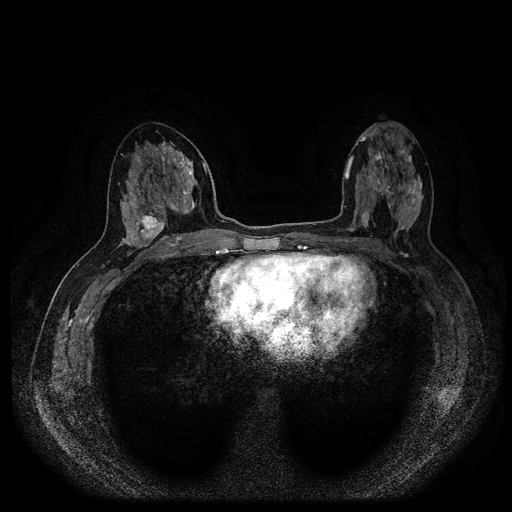
Breast MRI (dynamic contrast-enhanced, multi-phase), one axial slice; dynamic contrast-enhanced series, time point 2 of 5 at this slice position (early post-contrast); 1.5 T; TE 2.6 ms, TR 5.4 ms; 2 mm slice thickness; 512 × 512 image matrix, field of view 340 × 340 mm. Patient: female, 48 years.
Structures marked on this image (semi-automatic segmentation, software-assisted and operator-edited):
- breast lesion (labelled 'tumour' in the annotation; benign lesions carry a separate 'benign' label): box from (x=136, y=211) to (x=167, y=247) px